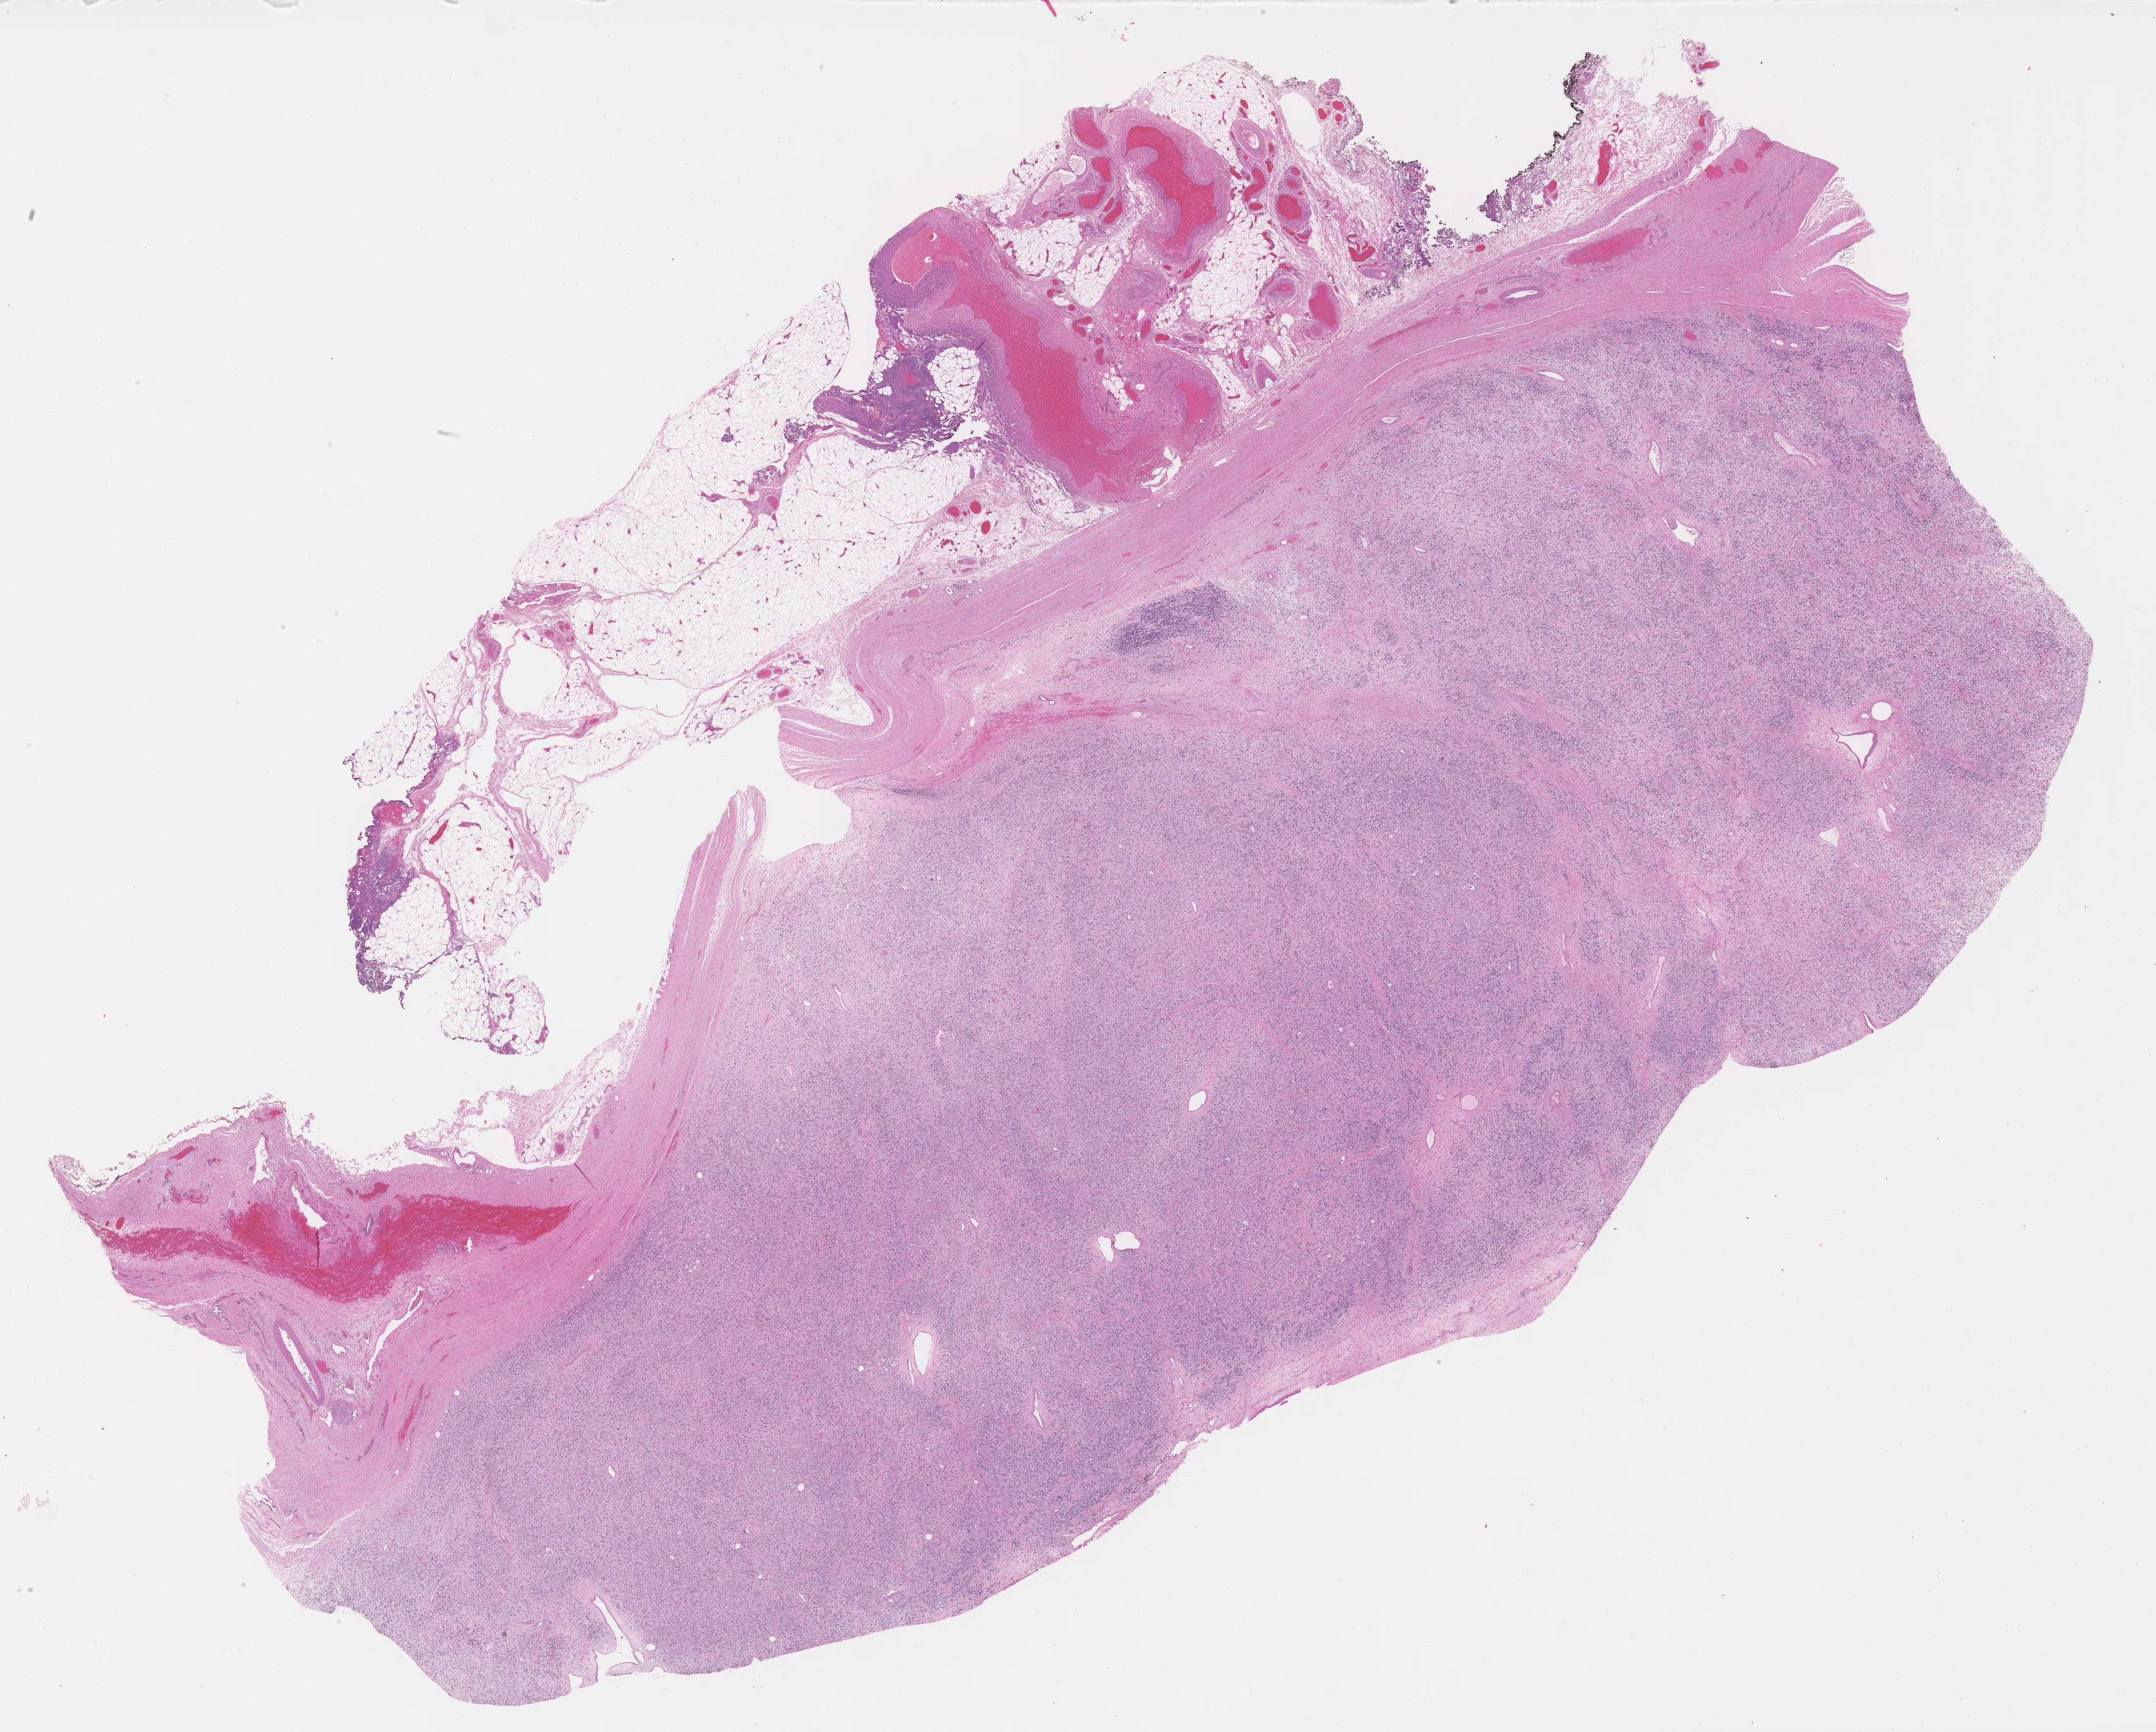
Haematoxylin and eosin whole-slide image of tumor tissue, a low-resolution overview of the entire scanned area, about 27.7 x 22.2 mm. Formalin-fixed paraffin-embedded section. Patient: male, age 20.2 years at diagnosis.
Diagnosis: rhabdomyosarcoma; histological classification: embryonal rhabdomyosarcoma. Metastatic status at presentation (as recorded): non-metastatic. Stage (as recorded): 1.